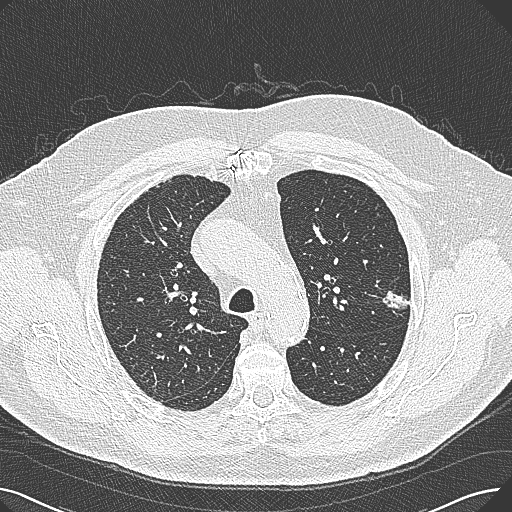
Axial slice from a low-dose chest CT screening exam. Baseline screening round. Lung window (W 1500 / L -600 HU). Slice 80 of 269 in the series. Male, age 74 years at enrolment.
Expert reader's lesion annotation, bounding box (x1, y1, x2, y2) in pixels: (373, 273, 424, 319). The exam's reader record, not a measurement of the box and not confirmed to be the same lesion: non-calcified nodule or mass ≥4 mm, left upper lobe, 15 × 10 mm, poorly defined margins, soft tissue attenuation. Participant outcome: lung cancer diagnosed 124 days after this screen — adenocarcinoma, NOS, left upper lobe, well differentiated (G1), stage IA (AJCC 6th edition), 26 mm at pathology.